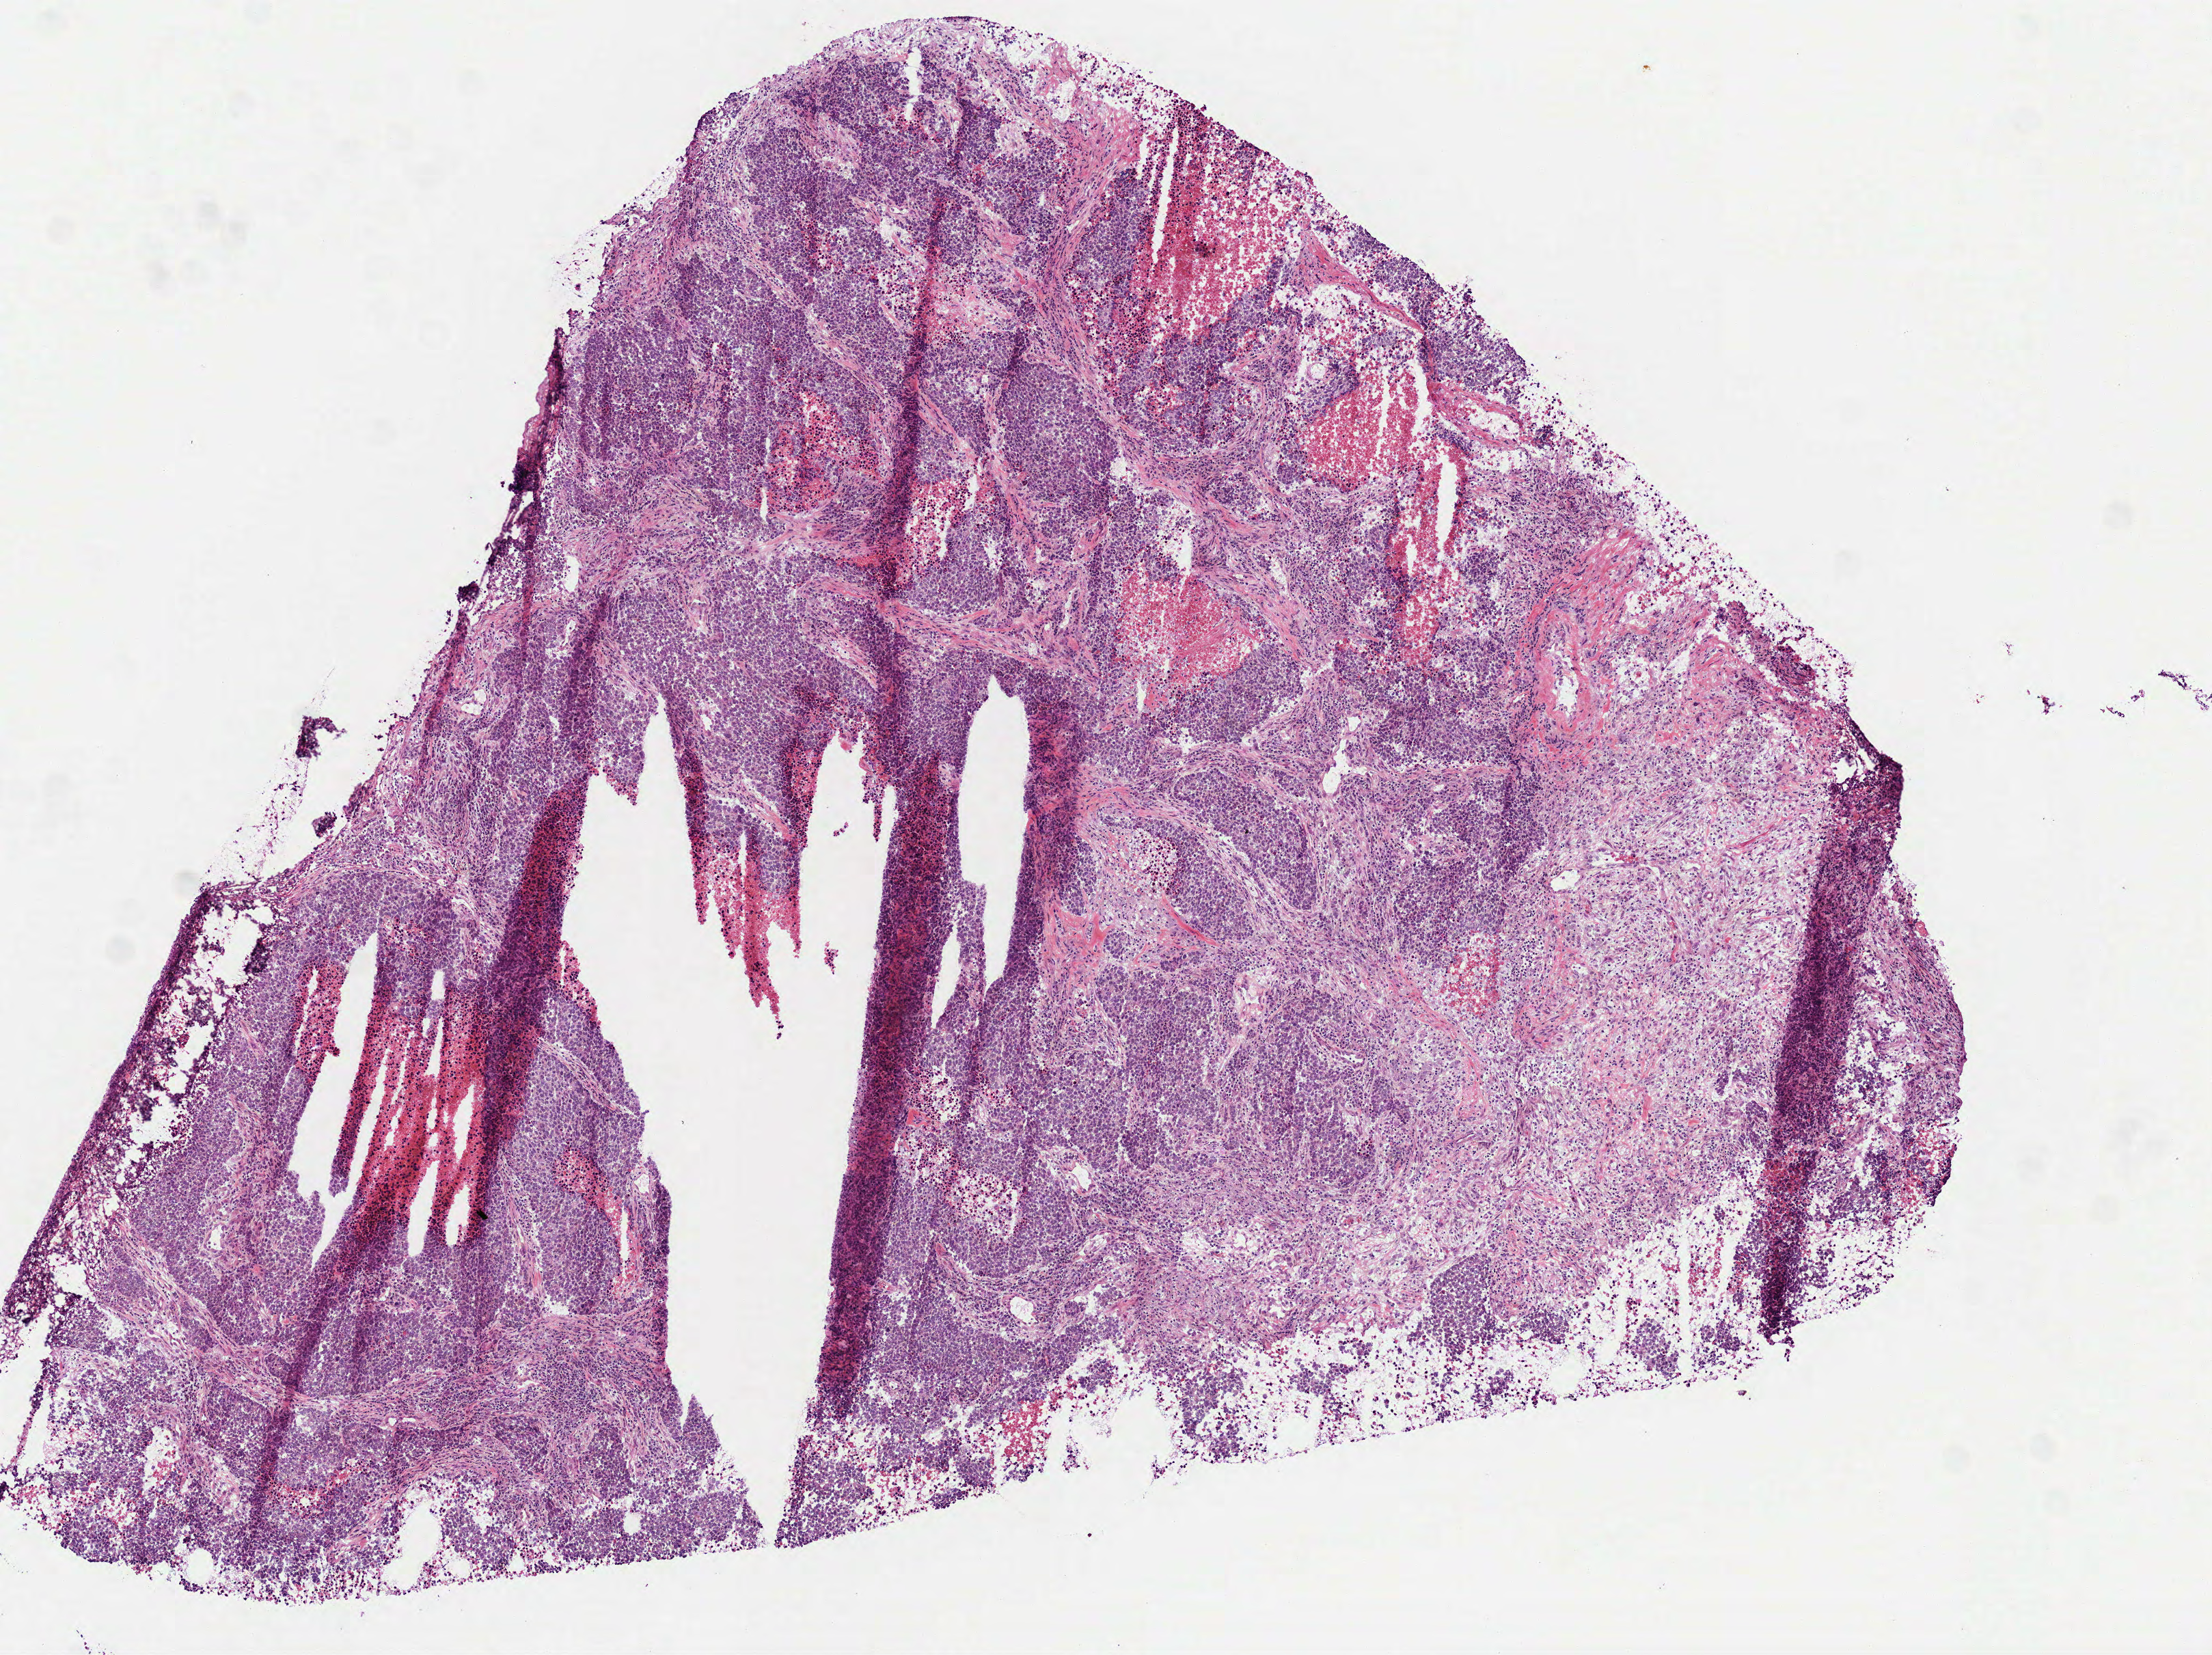
Whole-slide histology image, H&E-stained, low-resolution overview of the scanned area, about 6.5 x 4.9 mm (acquisition: 40x scan), frozen section from the top of the tissue portion, lung, primary tumour sample. Patient: female, age at initial diagnosis 76 years. Pathologist review of this section (percent, as recorded): tumour cells 70%, tumour nuclei 70%, normal cells 0%, stromal cells 15%, necrosis 15%.
Laterality: left. AJCC pathologic stage: IA (7th edition). Histologic diagnosis: Adenocarcinoma, NOS (lower lobe, lung).